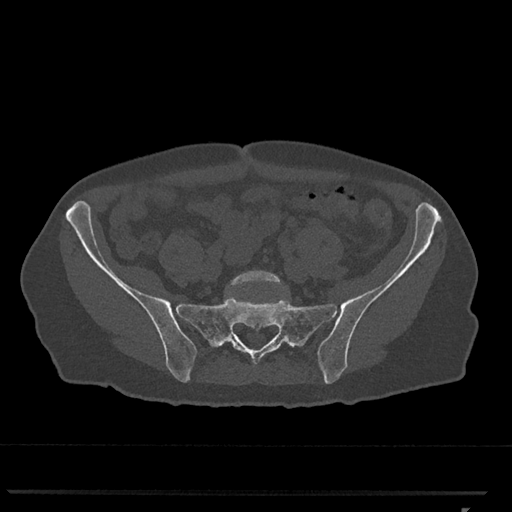
CT including the spine, one axial slice; position 108 of 793 along the scan axis; reconstruction kernel Br40s/3; 120 kVp; bone window (W 1800 / L 400 HU); 0.5 mm slice thickness; 512 × 512 image matrix. Patient: female, 62 years. From the clinical record (not read from this slice): primary cancer: renal.
Structures marked on this image (semi-automatic segmentation, software-assisted and operator-edited):
- L5 vertebra: bounding box (x1, y1, x2, y2) in pixels: (230, 270, 282, 288)